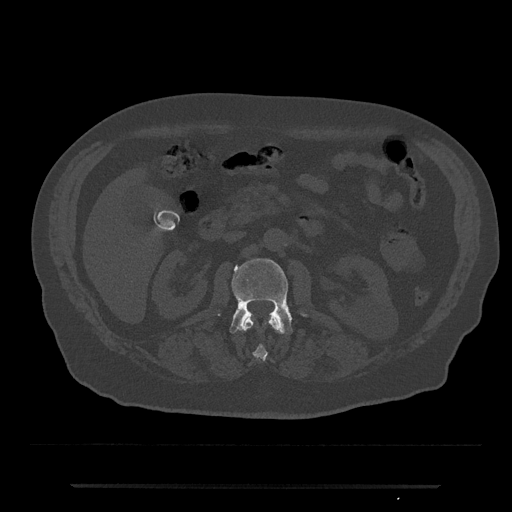
CT including the spine, one axial slice. Slice 491 of 797 in the series (ordered by position). Reconstruction kernel Br40s/3. 120 kVp. Bone window (W 1800 / L 400 HU). 0.5 mm slice thickness. 512 × 512 image matrix, field of view 434 × 434 mm. Male patient, age 80 years. Case-level facts recorded for this patient, not image findings: primary cancer: prostate.
Structures marked on this image (semi-automatic segmentation, software-assisted and operator-edited):
- L1 vertebra: bounding box (x1, y1, x2, y2) in pixels: (242, 316, 282, 361)
- L2 vertebra: (229, 258, 307, 334)